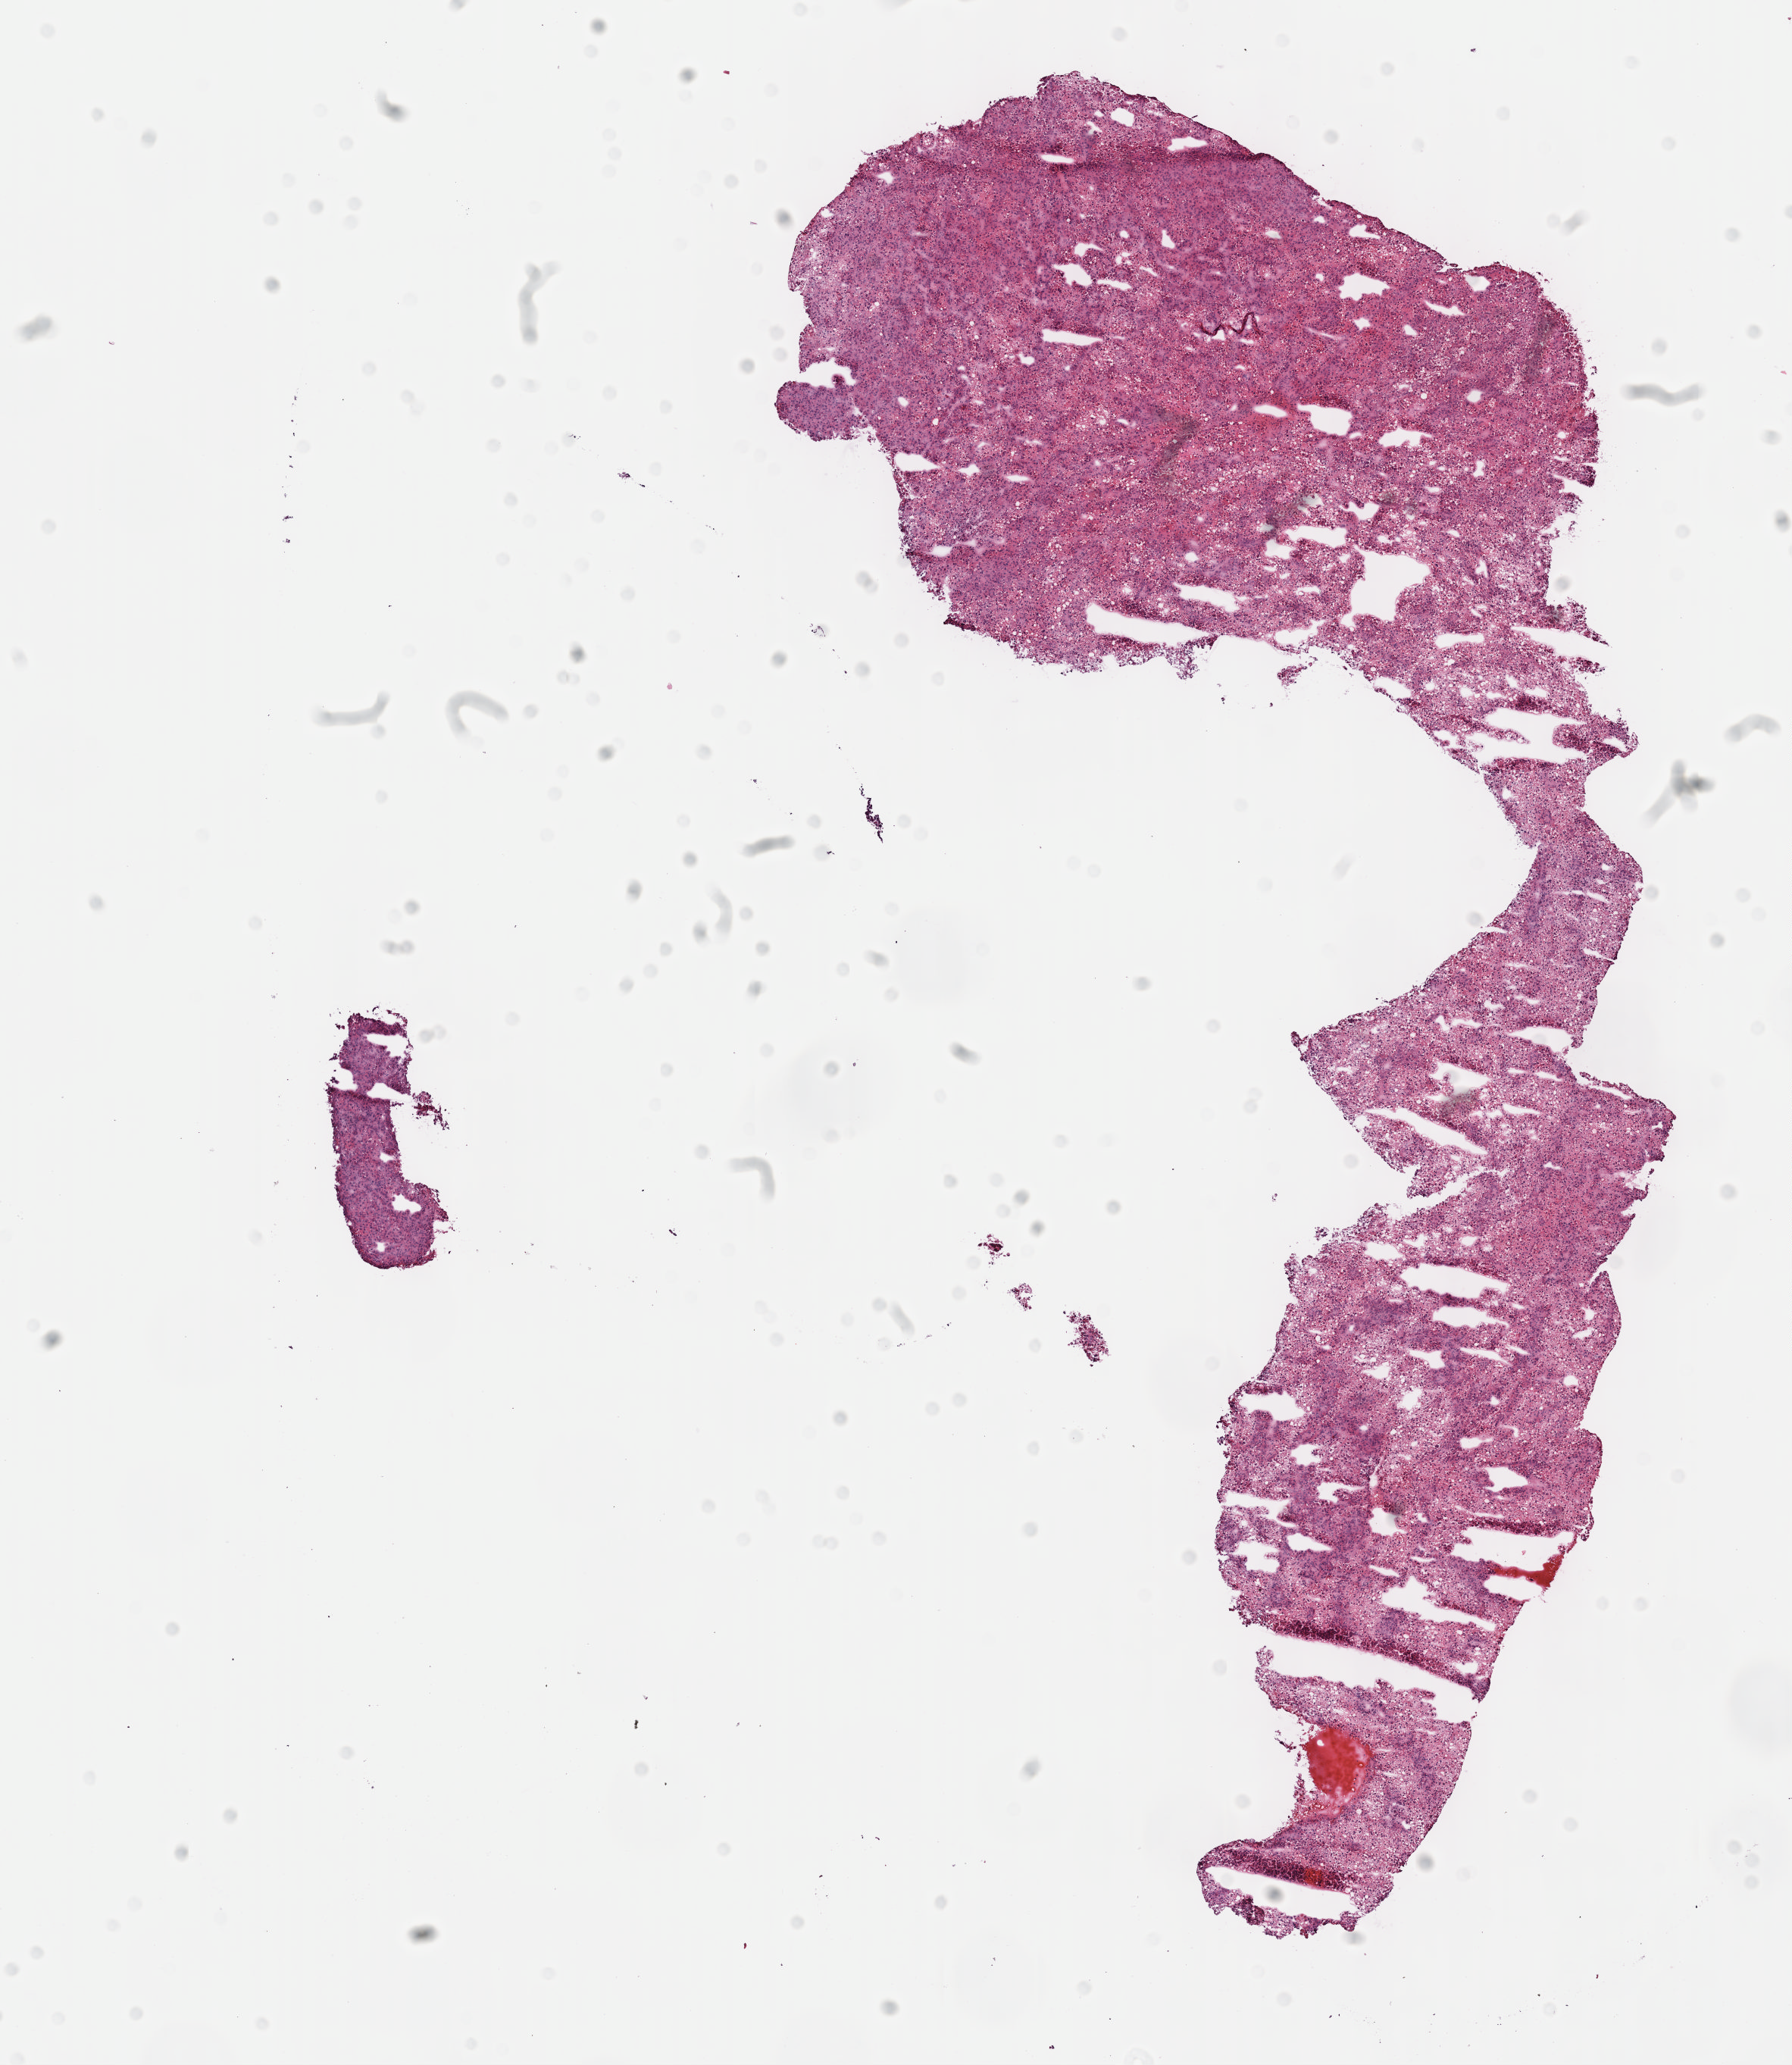
H&E-stained whole-slide image — shown as a low-resolution overview of the whole scanned area (about 9.6 x 11.0 mm, acquisition: 40x scan), frozen section, primary tumour sample from the liver. Patient: male, age at initial diagnosis 51 years. Histologic grade: G4 (undifferentiated). Pathologist review of this section (percent, as recorded): tumour cells 90%, tumour nuclei 95%, normal cells 0%, stromal cells 10%, necrosis 0%. Inflammatory infiltration, as recorded: lymphocyte infiltration 0%, monocyte infiltration 0%, neutrophil infiltration 0%.
- AJCC pathologic stage: I
- diagnosis: Hepatocellular carcinoma, NOS